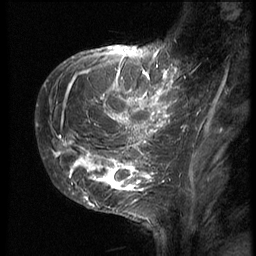
Breast MRI (dynamic contrast-enhanced), one sagittal slice; position 15 of 62 along the scan axis; 3 images stored at this slice position (order not interpretable as contrast timing); 1.5 T; TE 4.2 ms, TR 9 ms; 2.5 mm slice thickness; 256 × 256 image matrix, field of view 180 × 180 mm. Patient: female, 28 years. Case-level facts recorded for this patient, not image findings: setting: breast cancer imaged before/during neoadjuvant chemotherapy.
Outlined on this slice (semi-automatically segmented with operator editing):
- analysis volume of interest (the breast-tissue region the enhancement analysis was run in; not a lesion): bounding box <42,63,192,207> (left, top, right, bottom; pixels)
- tumour enhancement mask (voxels above the 140 % enhancement threshold inside the analysis volume of interest): <52,65,180,198>